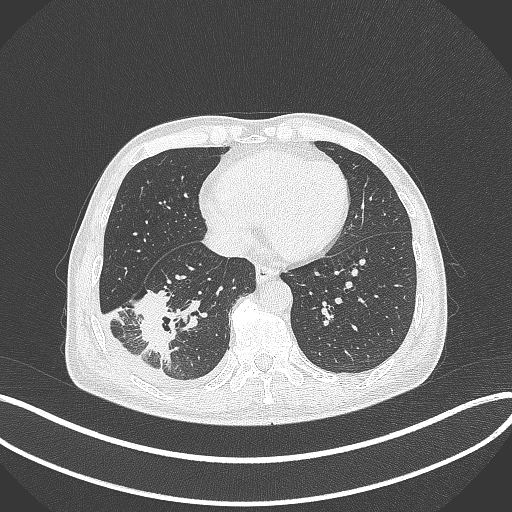
Chest CT, one axial slice; reconstruction kernel B70f; lung window (W 1500 / L -600 HU); 512 × 512 image matrix. Patient: male, 64 years. From the clinical record (not read from this slice): clinical TNM (as recorded): T3 N0 M0; histopathological grade: G2-3.
Annotated regions visible in this slice (bounding box drawn by a radiologist):
- lung tumour (recorded histology: adenocarcinoma): bounding box <131,280,185,367> (left, top, right, bottom; pixels)